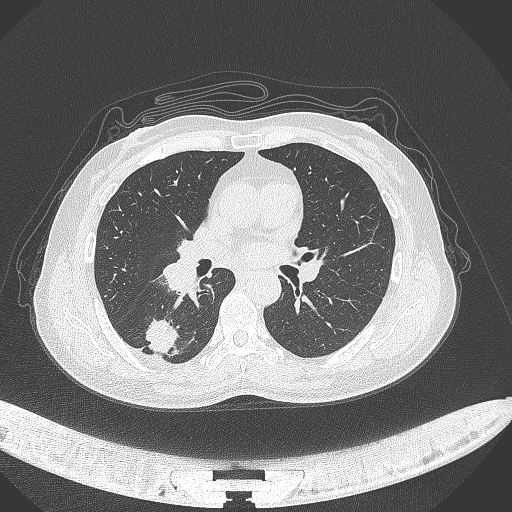
Chest CT, one axial slice; slice 164 of 352 in the series (ordered by position); lung window (W 1500 / L -600 HU); 512 × 512 image matrix, field of view 400 × 400 mm. Patient: female, 55 years. Case-level facts recorded for this patient, not image findings: clinical TNM (as recorded): T1c N1 M0.
Structures marked on this image (rectangle marked by the reading radiologist):
- lung tumour (recorded histology: adenocarcinoma): box from (x=140, y=313) to (x=181, y=357) px